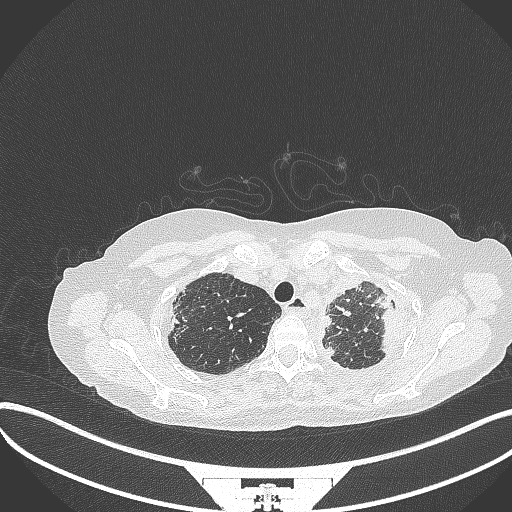
Chest CT, one axial slice; position 289 of 373 along the scan axis; reconstruction kernel B70f; 120 kVp; lung window (W 1500 / L -600 HU); 1 mm slice thickness; 512 × 512 image matrix. Female patient, age 56 years. From the clinical record (not read from this slice): clinical TNM (as recorded): T1 N0 M0.
Outlined on this slice (rectangle marked by the reading radiologist):
- lung tumour (recorded histology: adenocarcinoma): box from (x=374, y=293) to (x=403, y=354) px